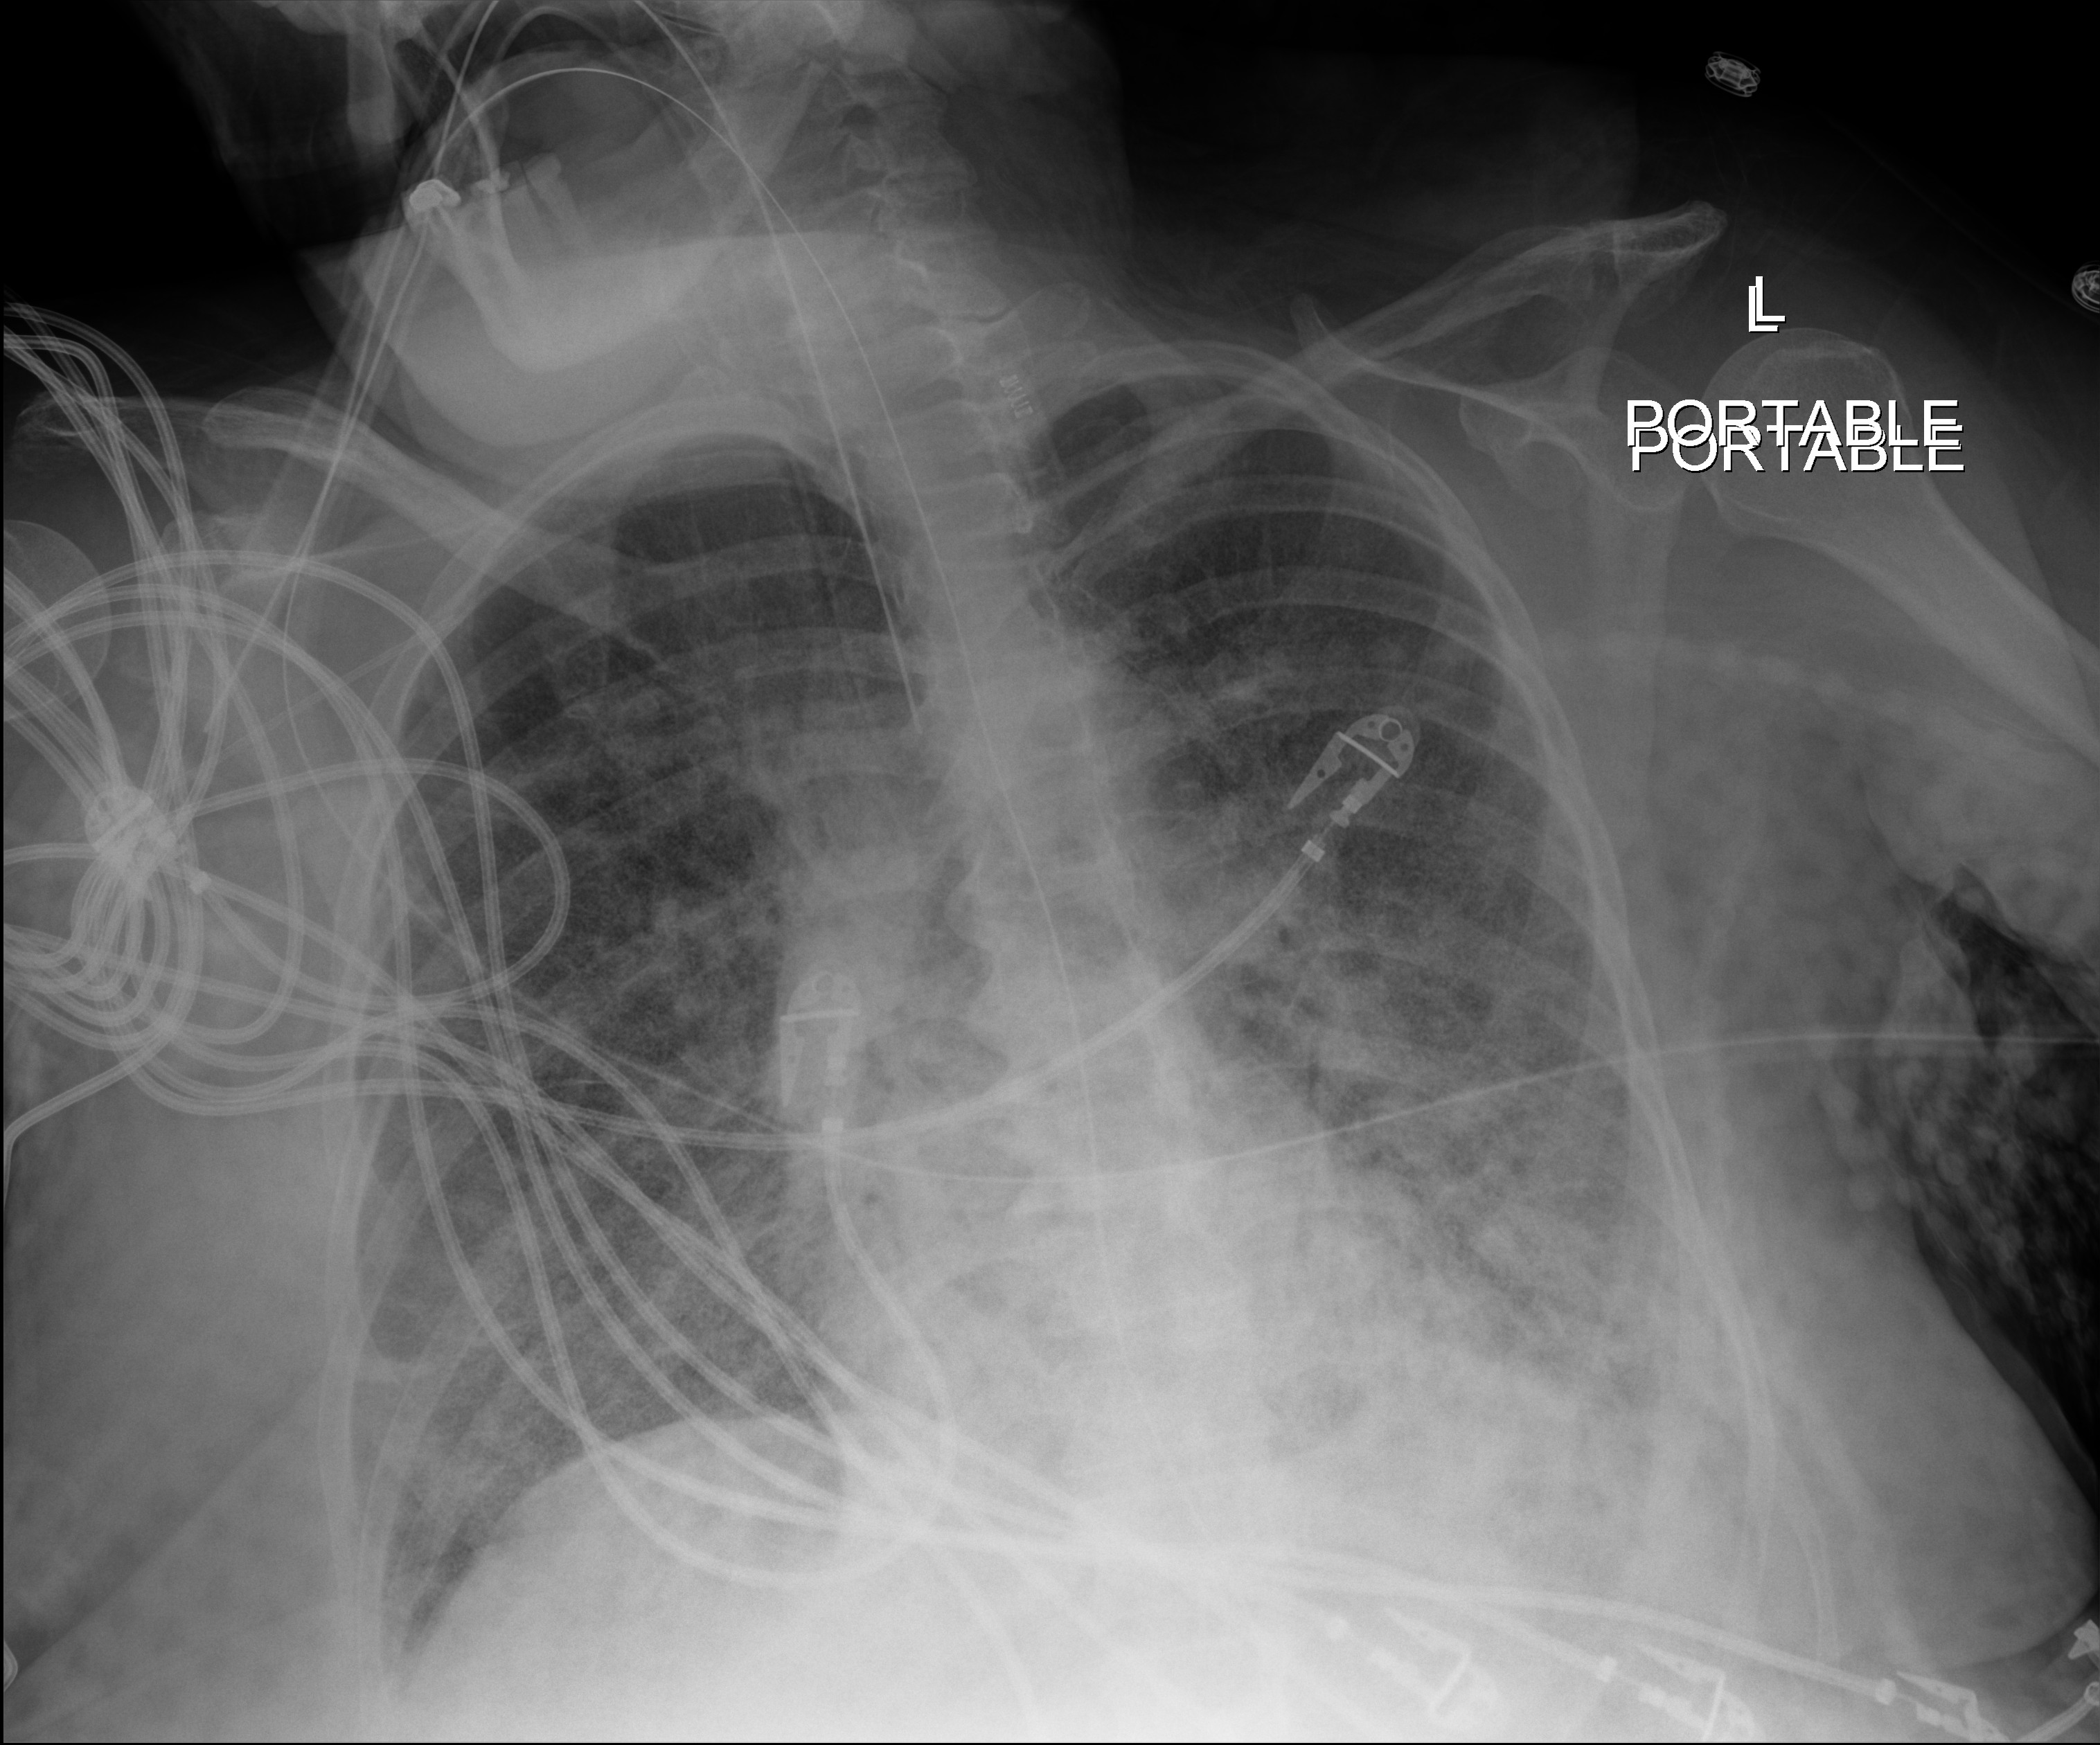
Bedside chest radiograph (digital radiography), anteroposterior (AP) projection. Patient hospitalised with COVID-19; female, aged 60–74 years.
Admission-level facts for this patient (not findings on this image; timing relative to this image not recorded): hypertension (admission record): no.